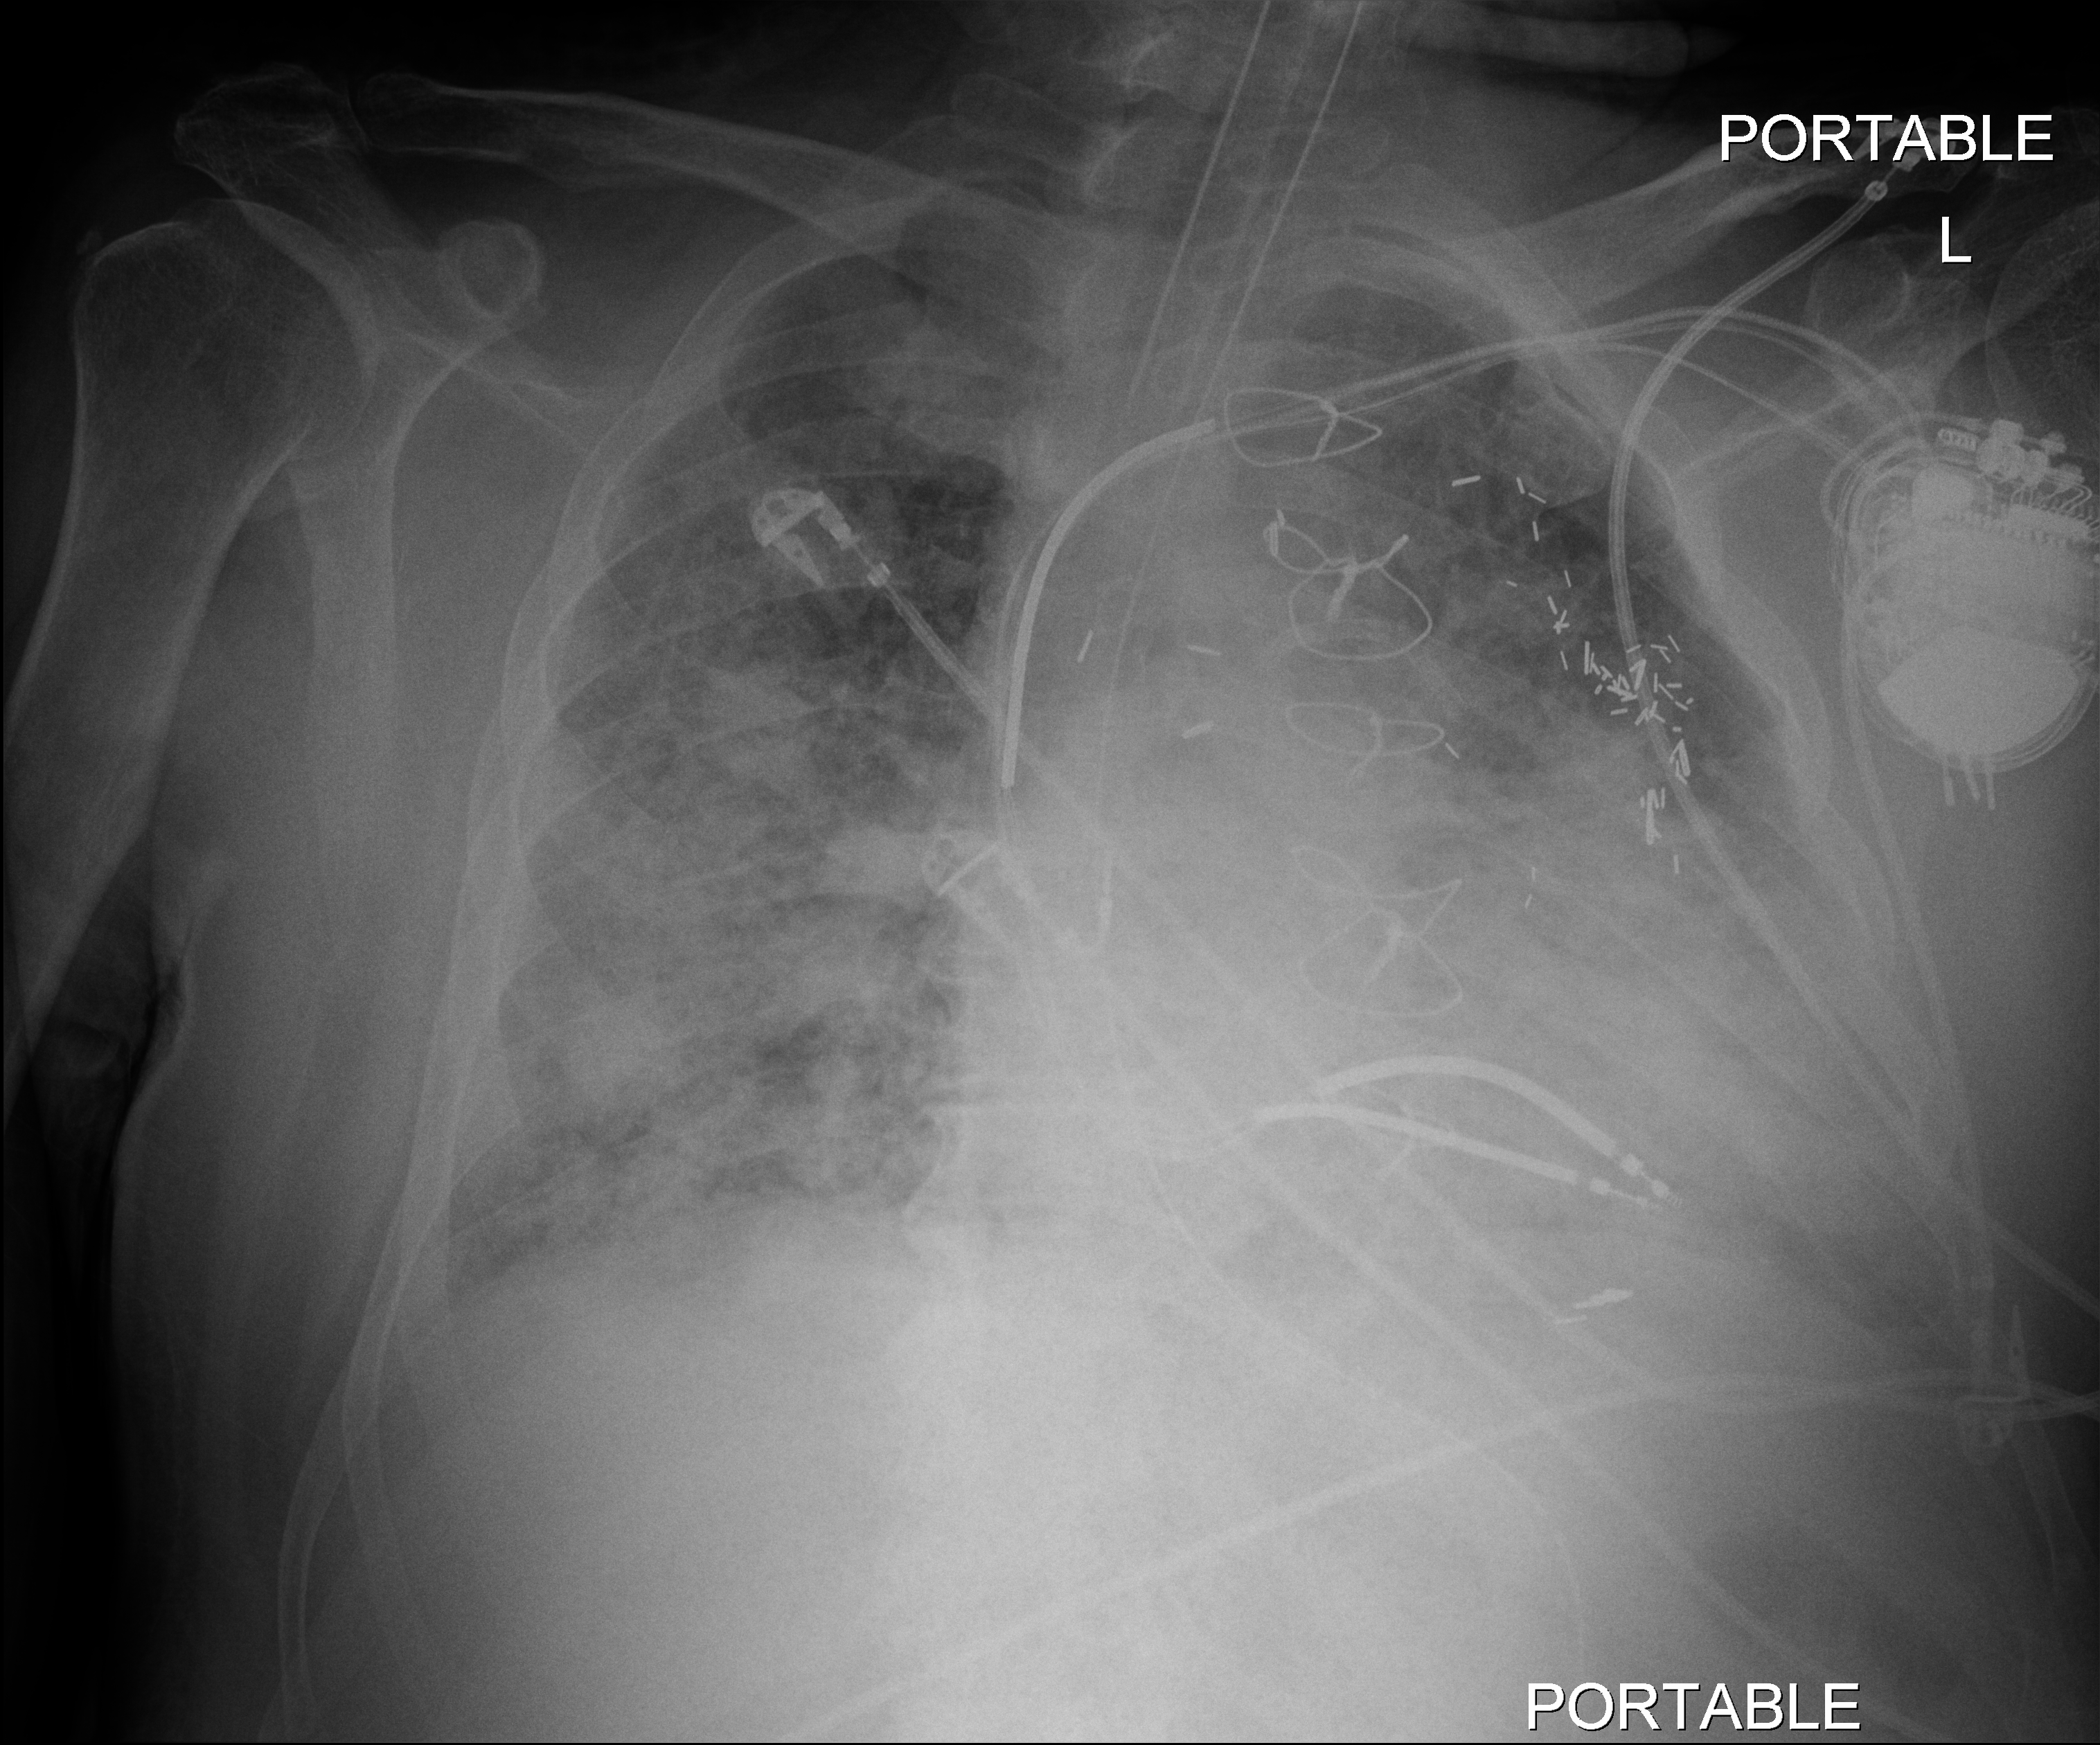
Chest radiograph; anteroposterior (AP) projection. Patient hospitalised with COVID-19; male, aged 60–74 years.
Admission-level facts for this patient (not findings on this image; timing relative to this image not recorded): other chronic lung disease (admission record): no.